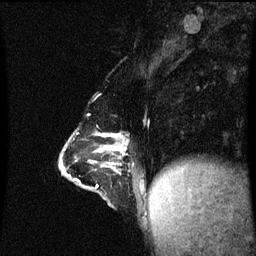
Breast MRI (dynamic contrast-enhanced), one sagittal slice; slice 23 of 60 in the series (ordered by position); dynamic contrast-enhanced series, image 2 of 3 at this slice position (ordered by acquisition); 1.5 T; TE 4.2 ms, TR 8.9 ms; 2 mm slice thickness; 256 × 256 image matrix, field of view 200 × 200 mm. Patient: female, 47 years. Case-level facts recorded for this patient, not image findings: setting: breast cancer imaged before/during neoadjuvant chemotherapy; receptor status: HR-positive, HER2-negative.
Structures marked on this image (semi-automatically segmented with operator editing):
- analysis volume of interest (the breast-tissue region the enhancement analysis was run in; not a lesion): box from (x=61, y=130) to (x=147, y=207) px
- tumour enhancement mask (voxels above the 70 % enhancement threshold inside the analysis volume of interest): (x=100, y=134)–(x=127, y=151)